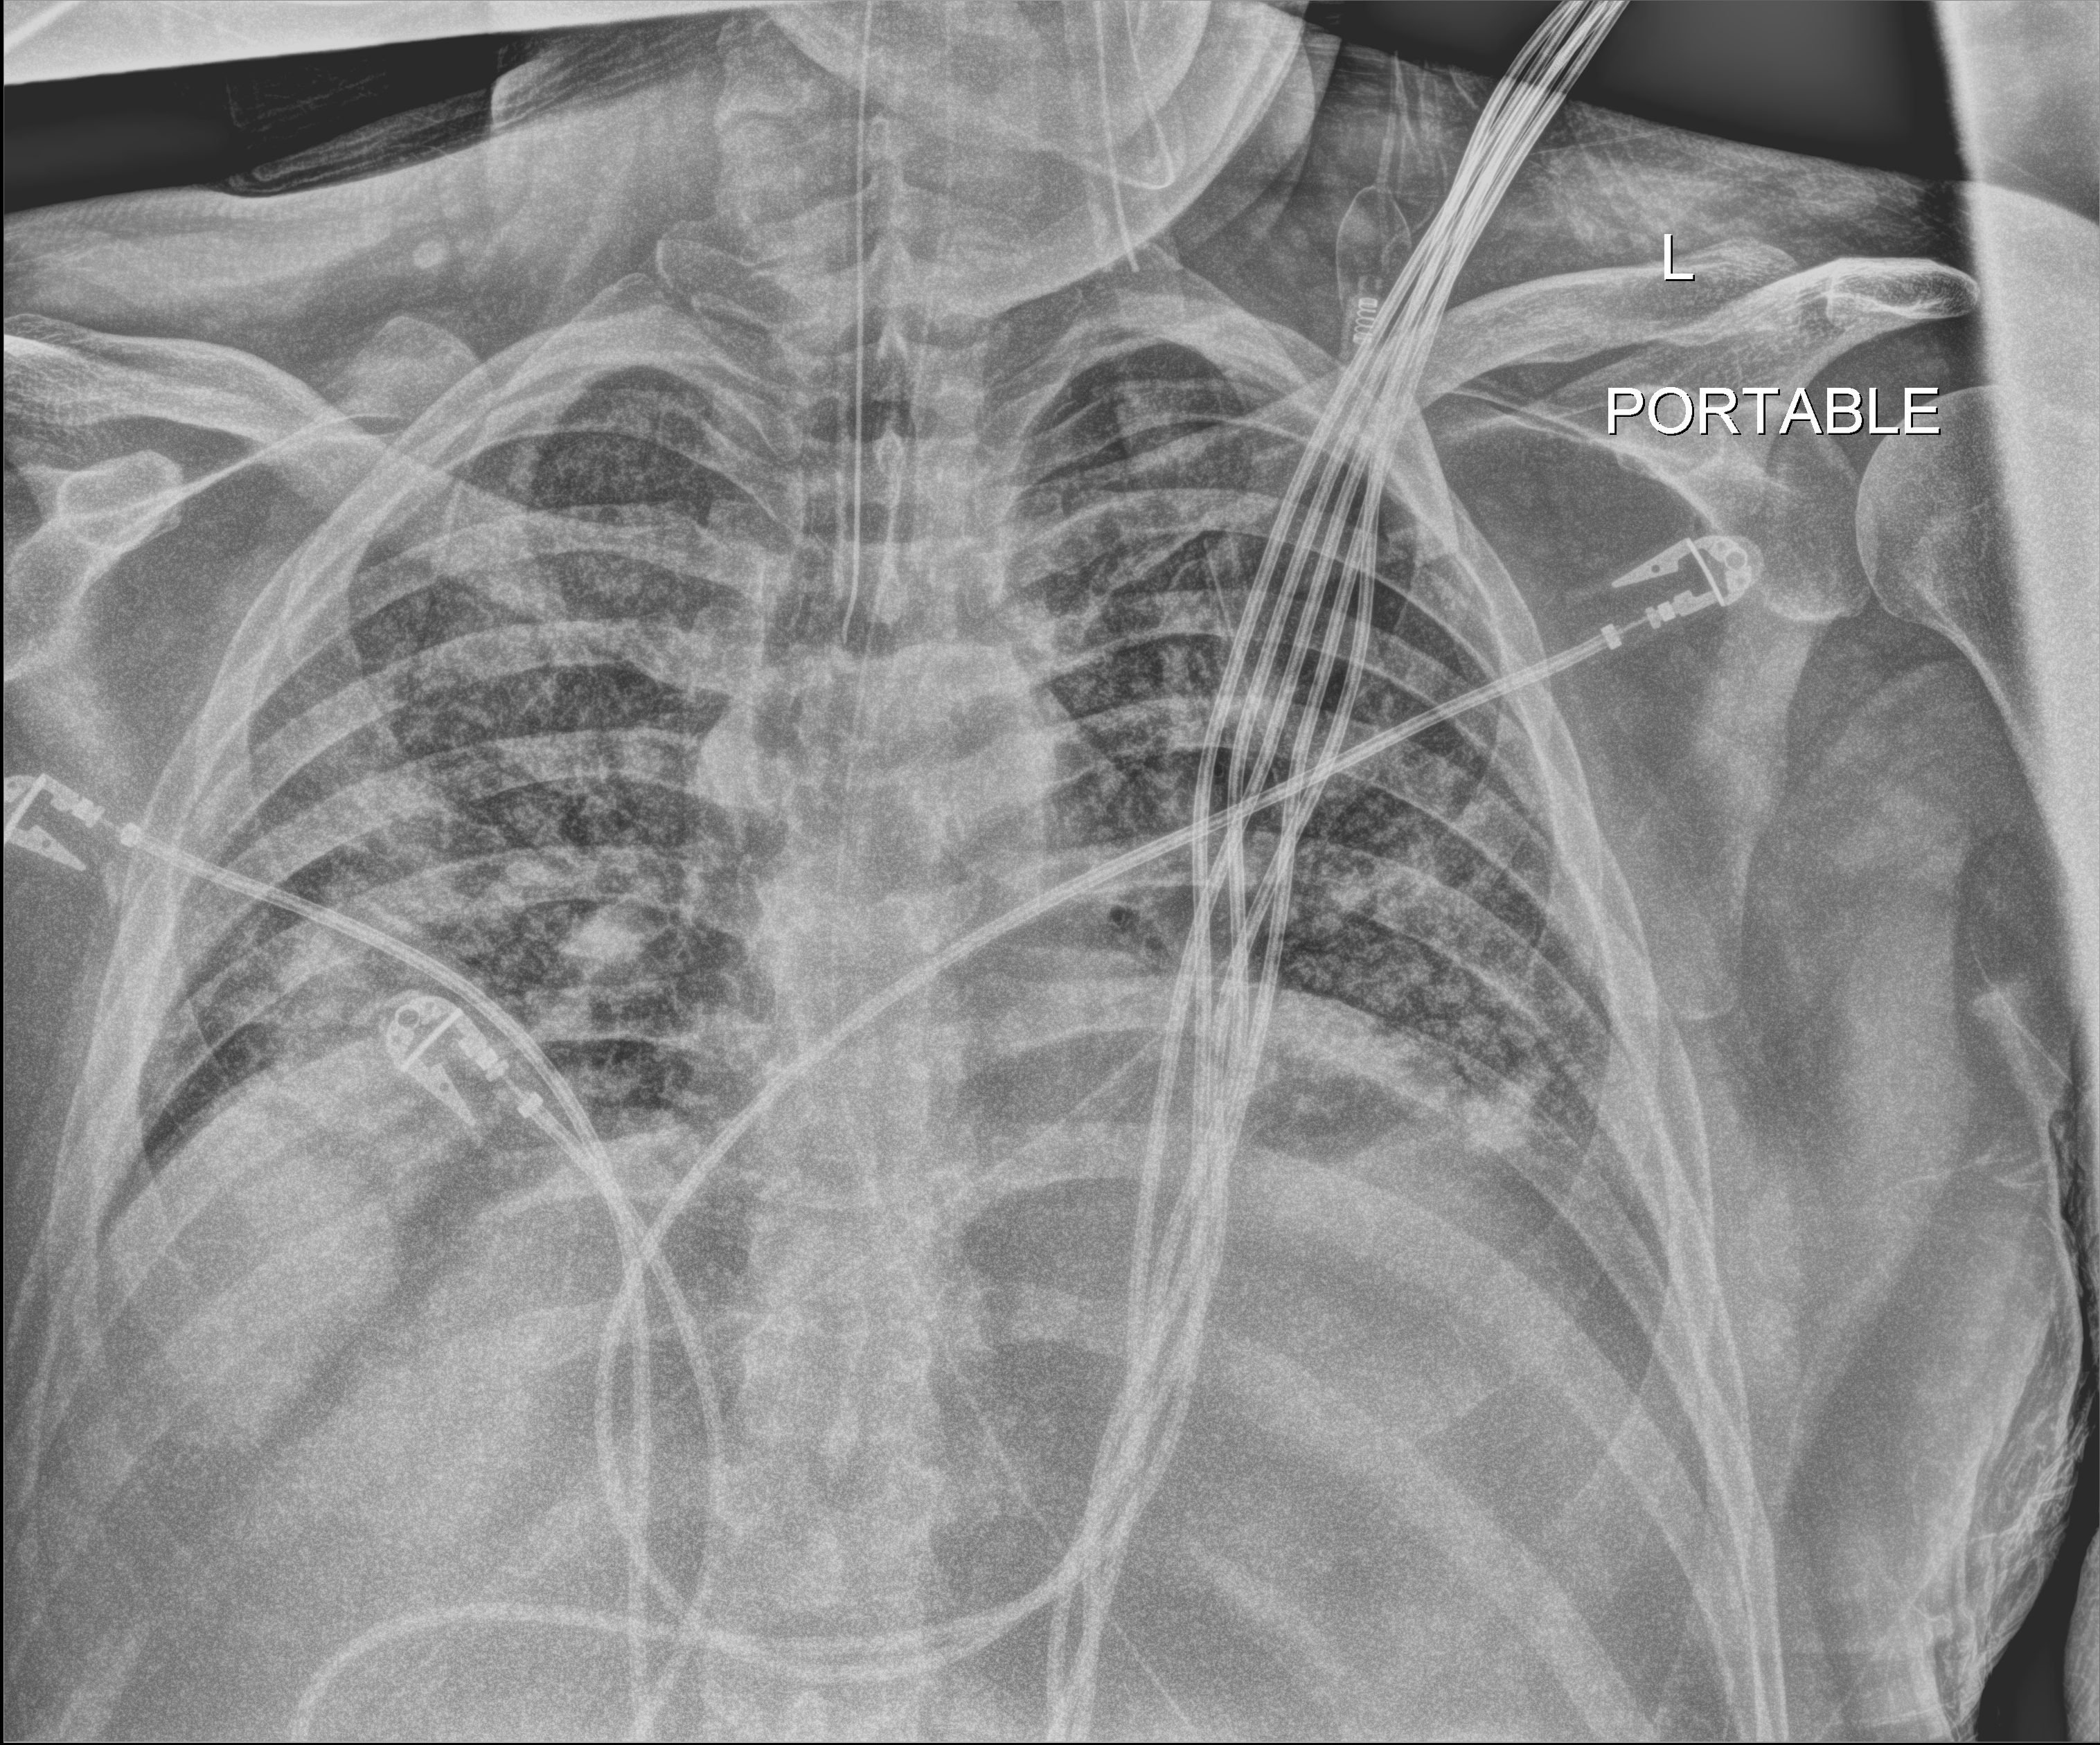
Bedside chest radiograph (digital radiography), anteroposterior (AP) projection. Male patient hospitalised with COVID-19, age 18–59 years.
Admission-level facts for this patient (not findings on this image; timing relative to this image not recorded):
- other chronic lung disease (admission record): no